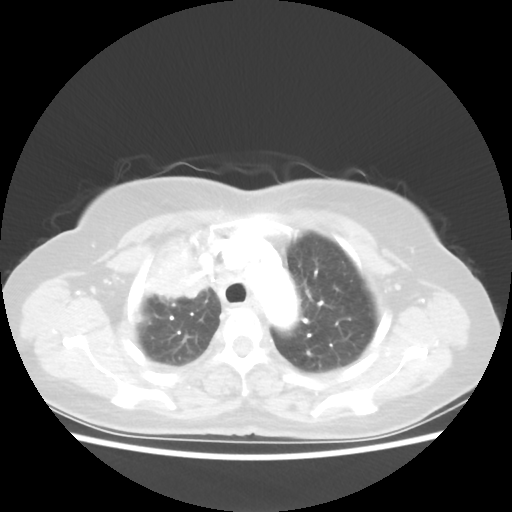
Chest CT, one axial slice; 80 kVp; lung window (W 1500 / L -600 HU); 512 × 512 image matrix. Patient: female, 62 years. Case-level facts recorded for this patient, not image findings: clinical TNM (as recorded): T4 N3 M0.
Annotated regions visible in this slice (bounding box drawn by a radiologist):
- lung tumour (recorded histology: squamous cell carcinoma): bounding box (x1, y1, x2, y2) in pixels: (135, 235, 217, 309)